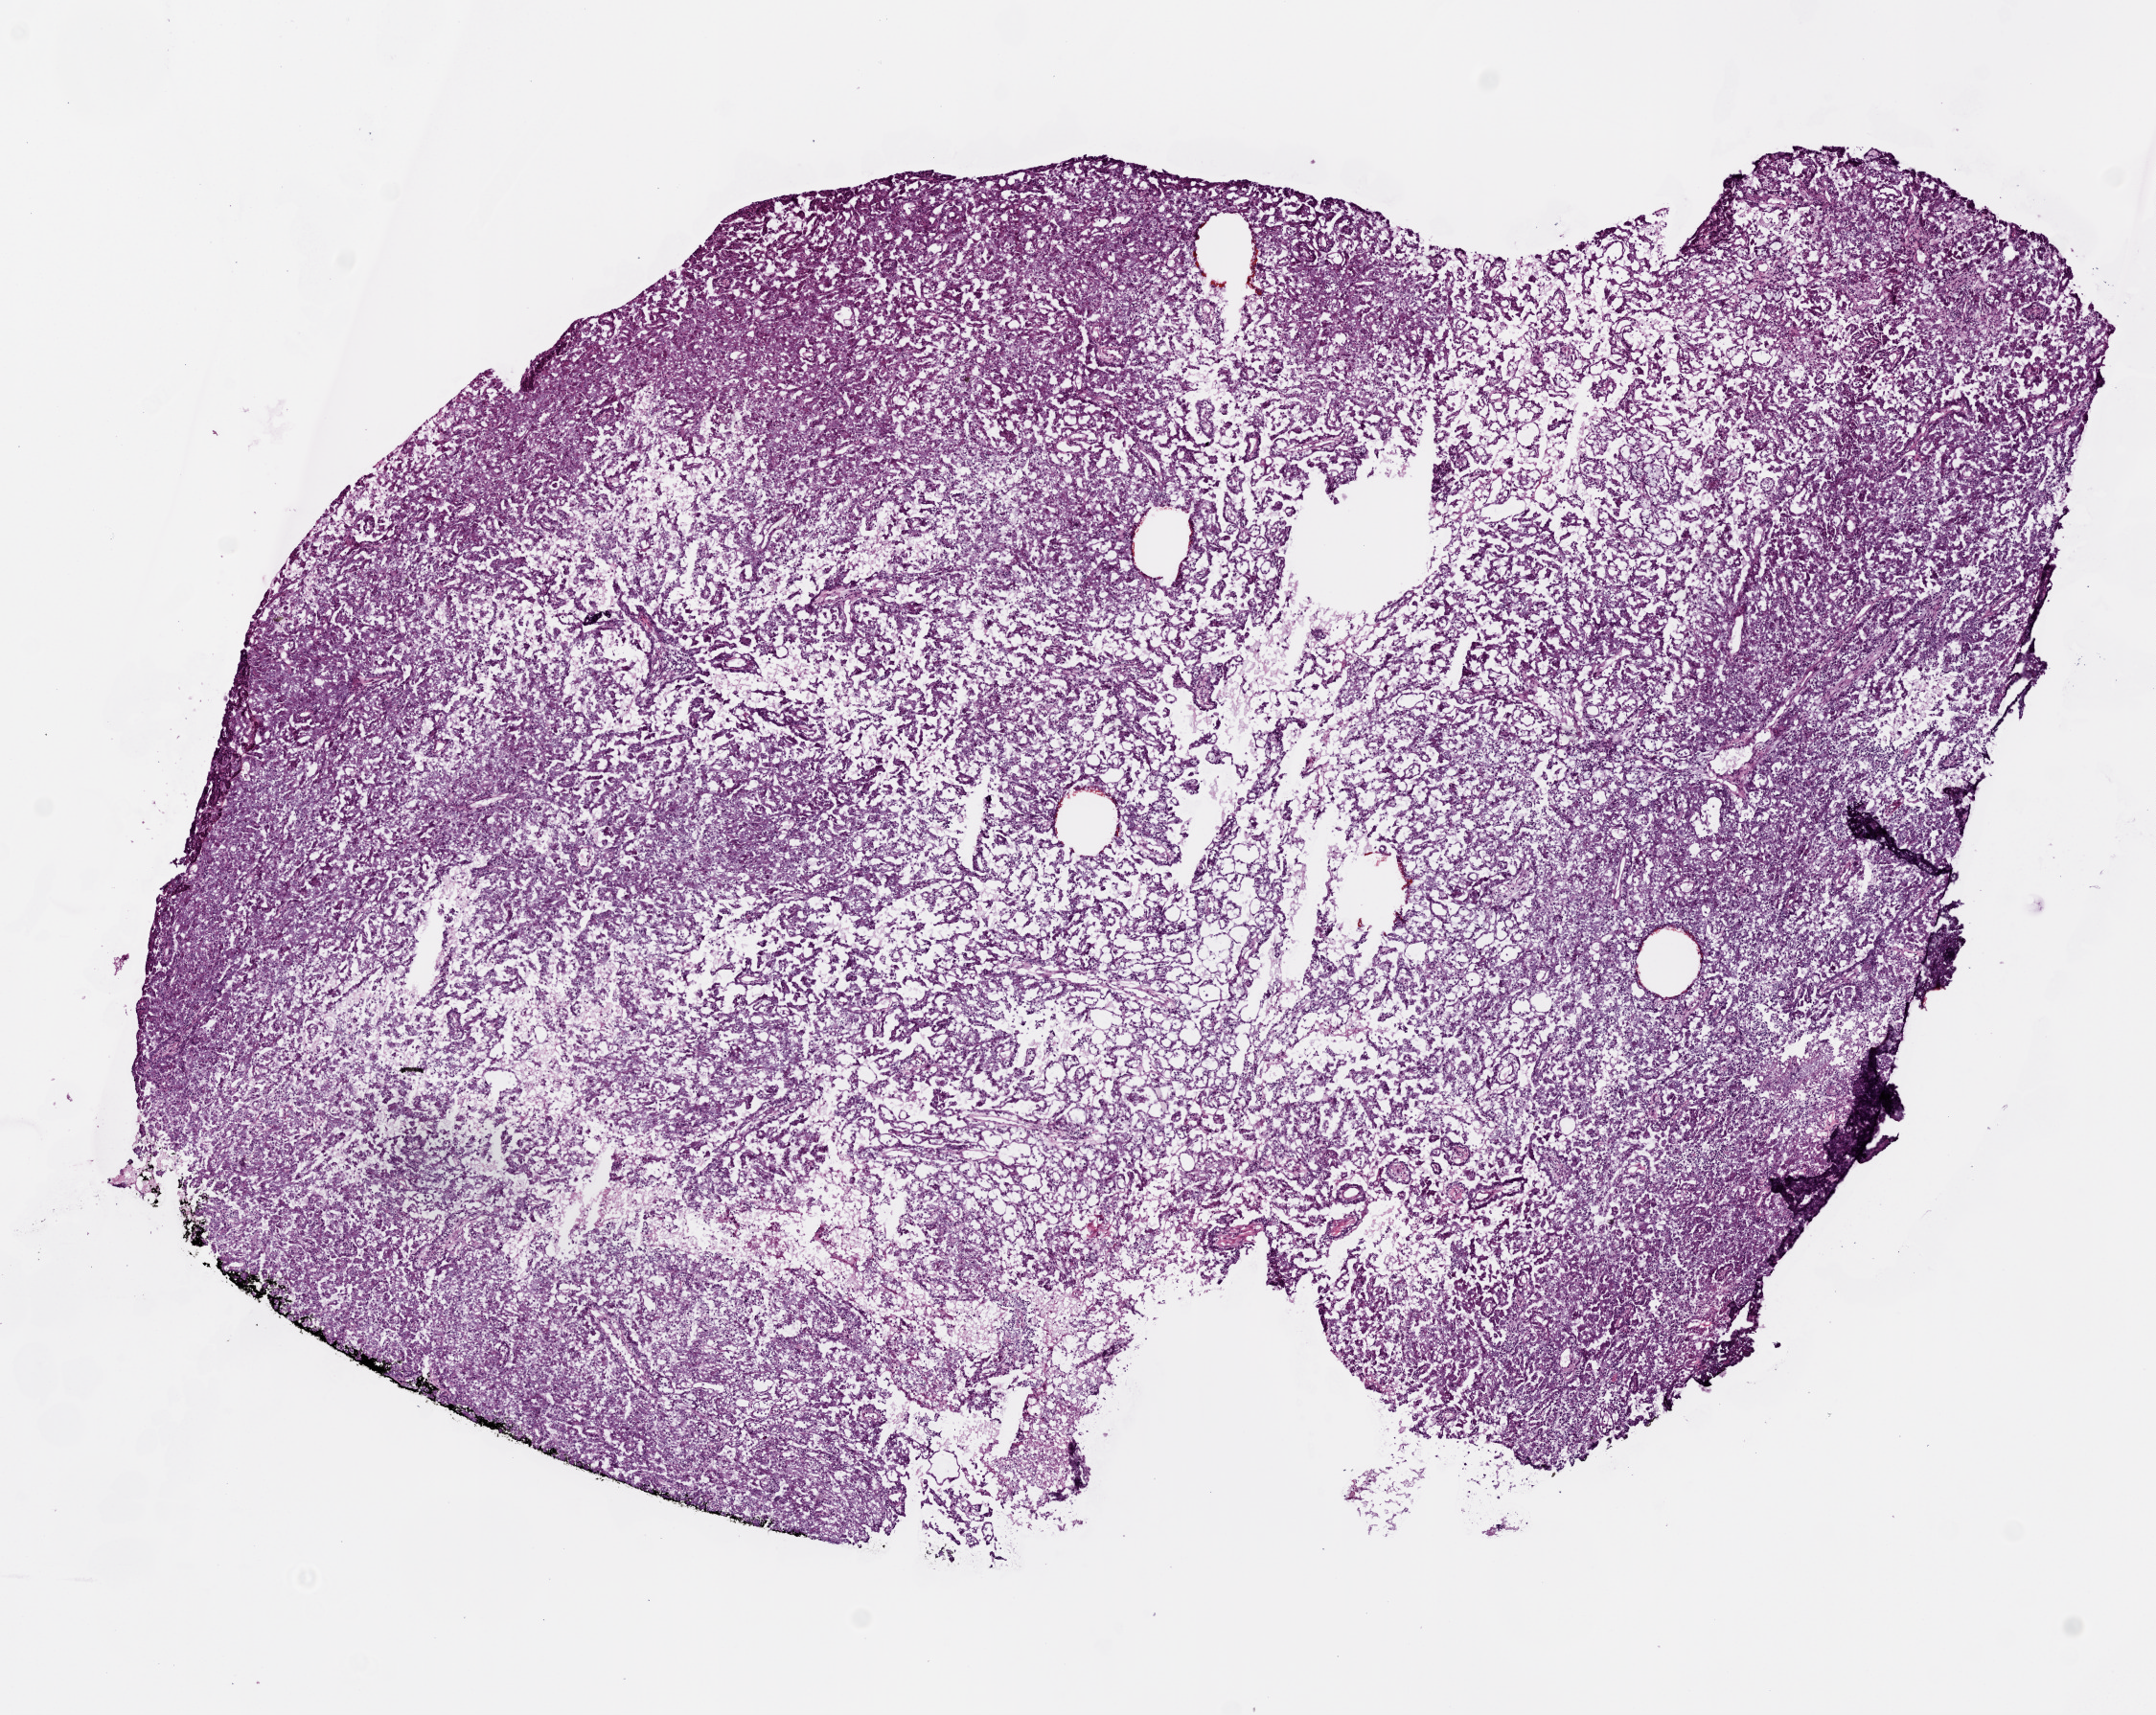
Whole-slide histology image, H&E — whole scanned area (about 9.0 x 7.2 mm) shown as a low-resolution overview. Frozen section from the top of the tissue portion. Sample: primary tumour, kidney. Patient: male, age at initial diagnosis 67 years. Composition of this section per pathologist review: tumour cells 100%, tumour nuclei 90%.
Histologic diagnosis: Papillary adenocarcinoma, NOS.